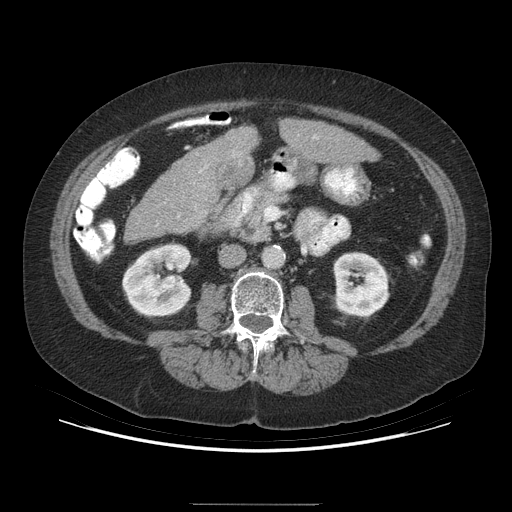
Contrast-enhanced abdominal CT (liver protocol), one axial slice; slice 133 of 192 in the series (ordered by position); 140 kVp; soft-tissue window (W 400 / L 40 HU); 512 × 512 image matrix, field of view 400 × 400 mm. From the clinical record (not read from this slice): diagnosis: hepatocellular carcinoma (patient treated with transarterial chemoembolisation; whether this scan precedes or follows treatment is not stated here); TNM stage (as recorded): Stage-I; Child-Pugh class: A.
Outlined on this slice (semi-automatically segmented with operator editing):
- liver parenchyma outside the tumour (the mass and vessels are separate outlines, so this box may not span the whole liver): bounding box (x1, y1, x2, y2) in pixels: (124, 119, 378, 241)
- mass: (216, 157, 255, 190)